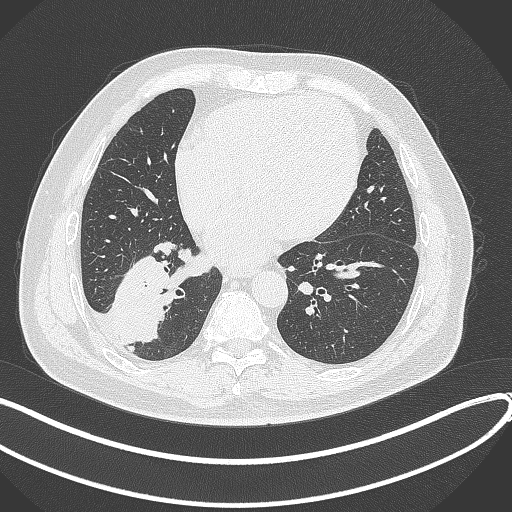
Chest CT, one axial slice; position 132 of 360 along the scan axis; lung window (W 1500 / L -600 HU); 512 × 512 image matrix. Male patient, age 59 years.
Annotated regions visible in this slice (bounding box drawn by a radiologist):
- lung tumour (recorded histology: adenocarcinoma): bounding box [x1, y1, x2, y2] px = [103, 249, 179, 343]